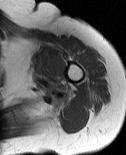
MRI of an extremity soft-tissue mass, one axial slice; MR volume resampled by the dataset authors to the PET/CT grid (not the native acquisition matrix); 3.27 mm slice thickness; 126 × 155 image matrix, field of view 123 × 151 mm. Female patient. Case-level facts recorded for this patient, not image findings: histological type: pleiomorphic leiomyosarcoma; grade: high; site of the primary tumour: left biceps.
Outlined on this slice (expert contour drawn on MRI and transferred to this co-registered scan by the dataset authors):
- gross tumour volume including surrounding oedema: box from (x=29, y=47) to (x=57, y=93) px
- gross tumour volume (mass): (x=38, y=58)–(x=53, y=73)